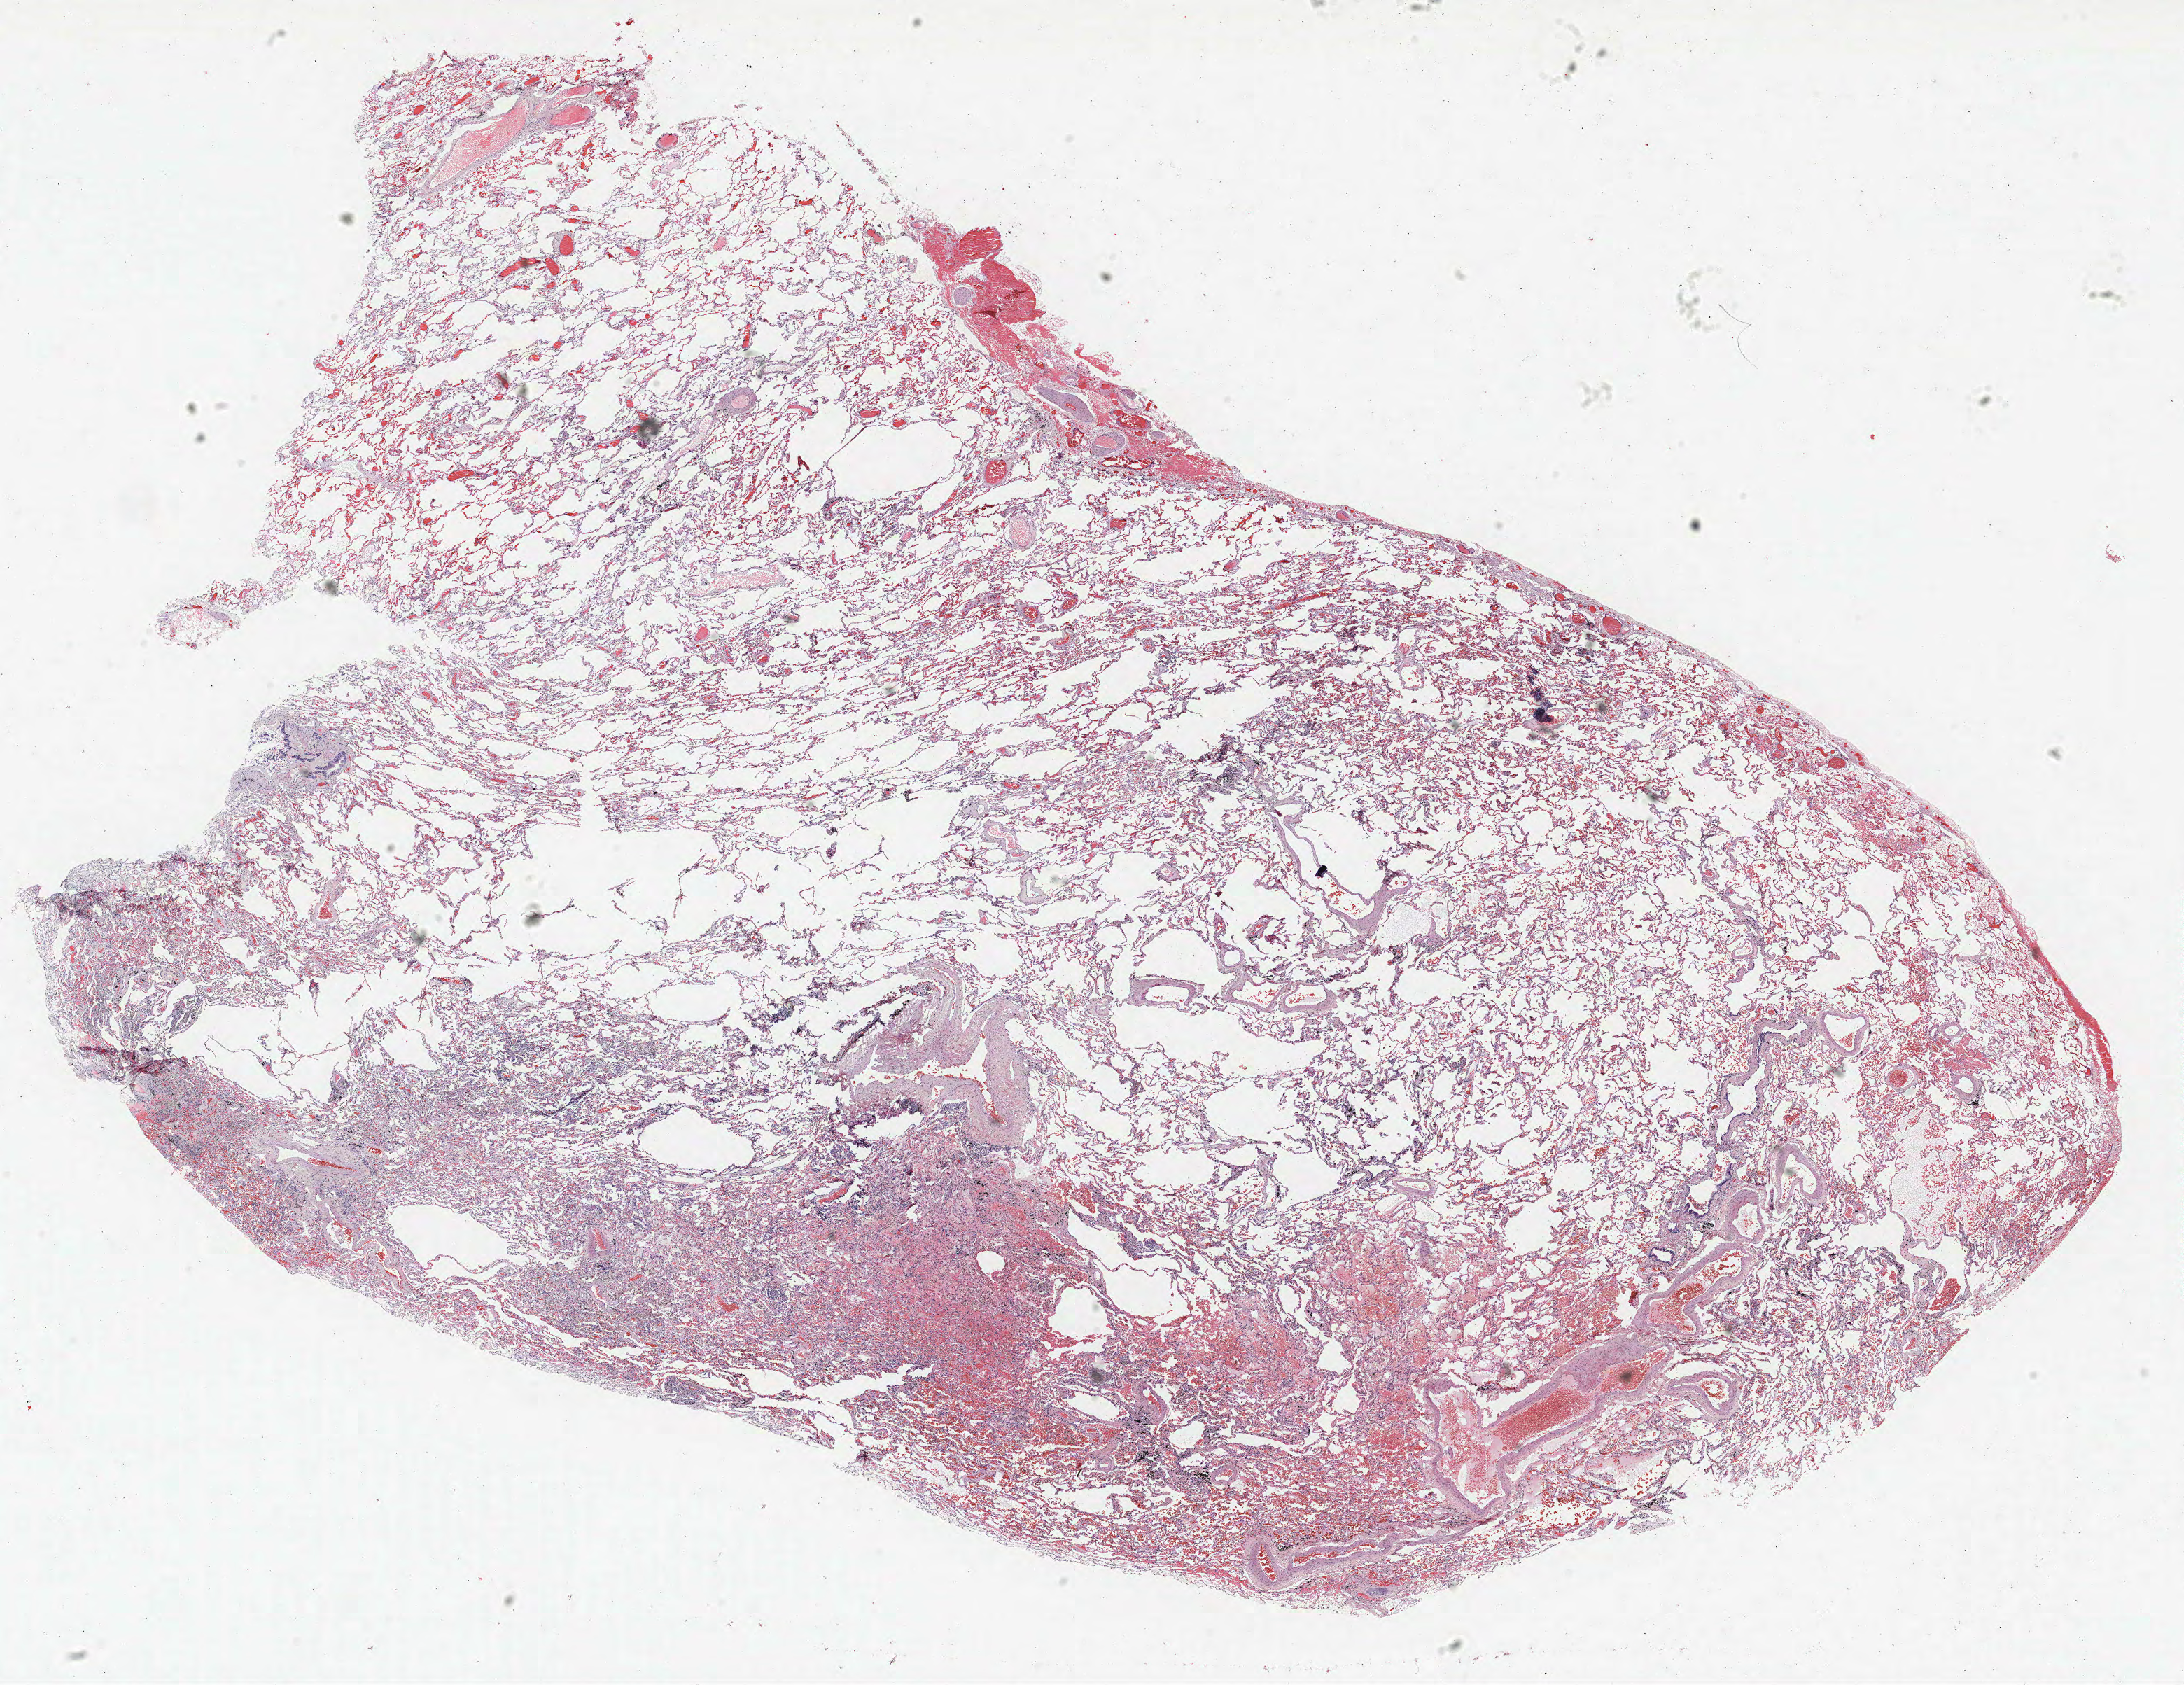
H&E-stained whole-slide image — whole scanned area (about 25.0 x 19.3 mm) shown as a low-resolution overview; formalin-fixed paraffin-embedded (FFPE) section; lung tissue. Male, age 71 at enrolment. Current smoker at enrolment. Grade: moderately differentiated (G2).
• primary tumour location (clinical record): left upper lobe
• tumour size (pathology): 10 mm
• participant's lung-cancer diagnosis: Adenocarcinoma, NOS
• stage (AJCC 6th edition): IA